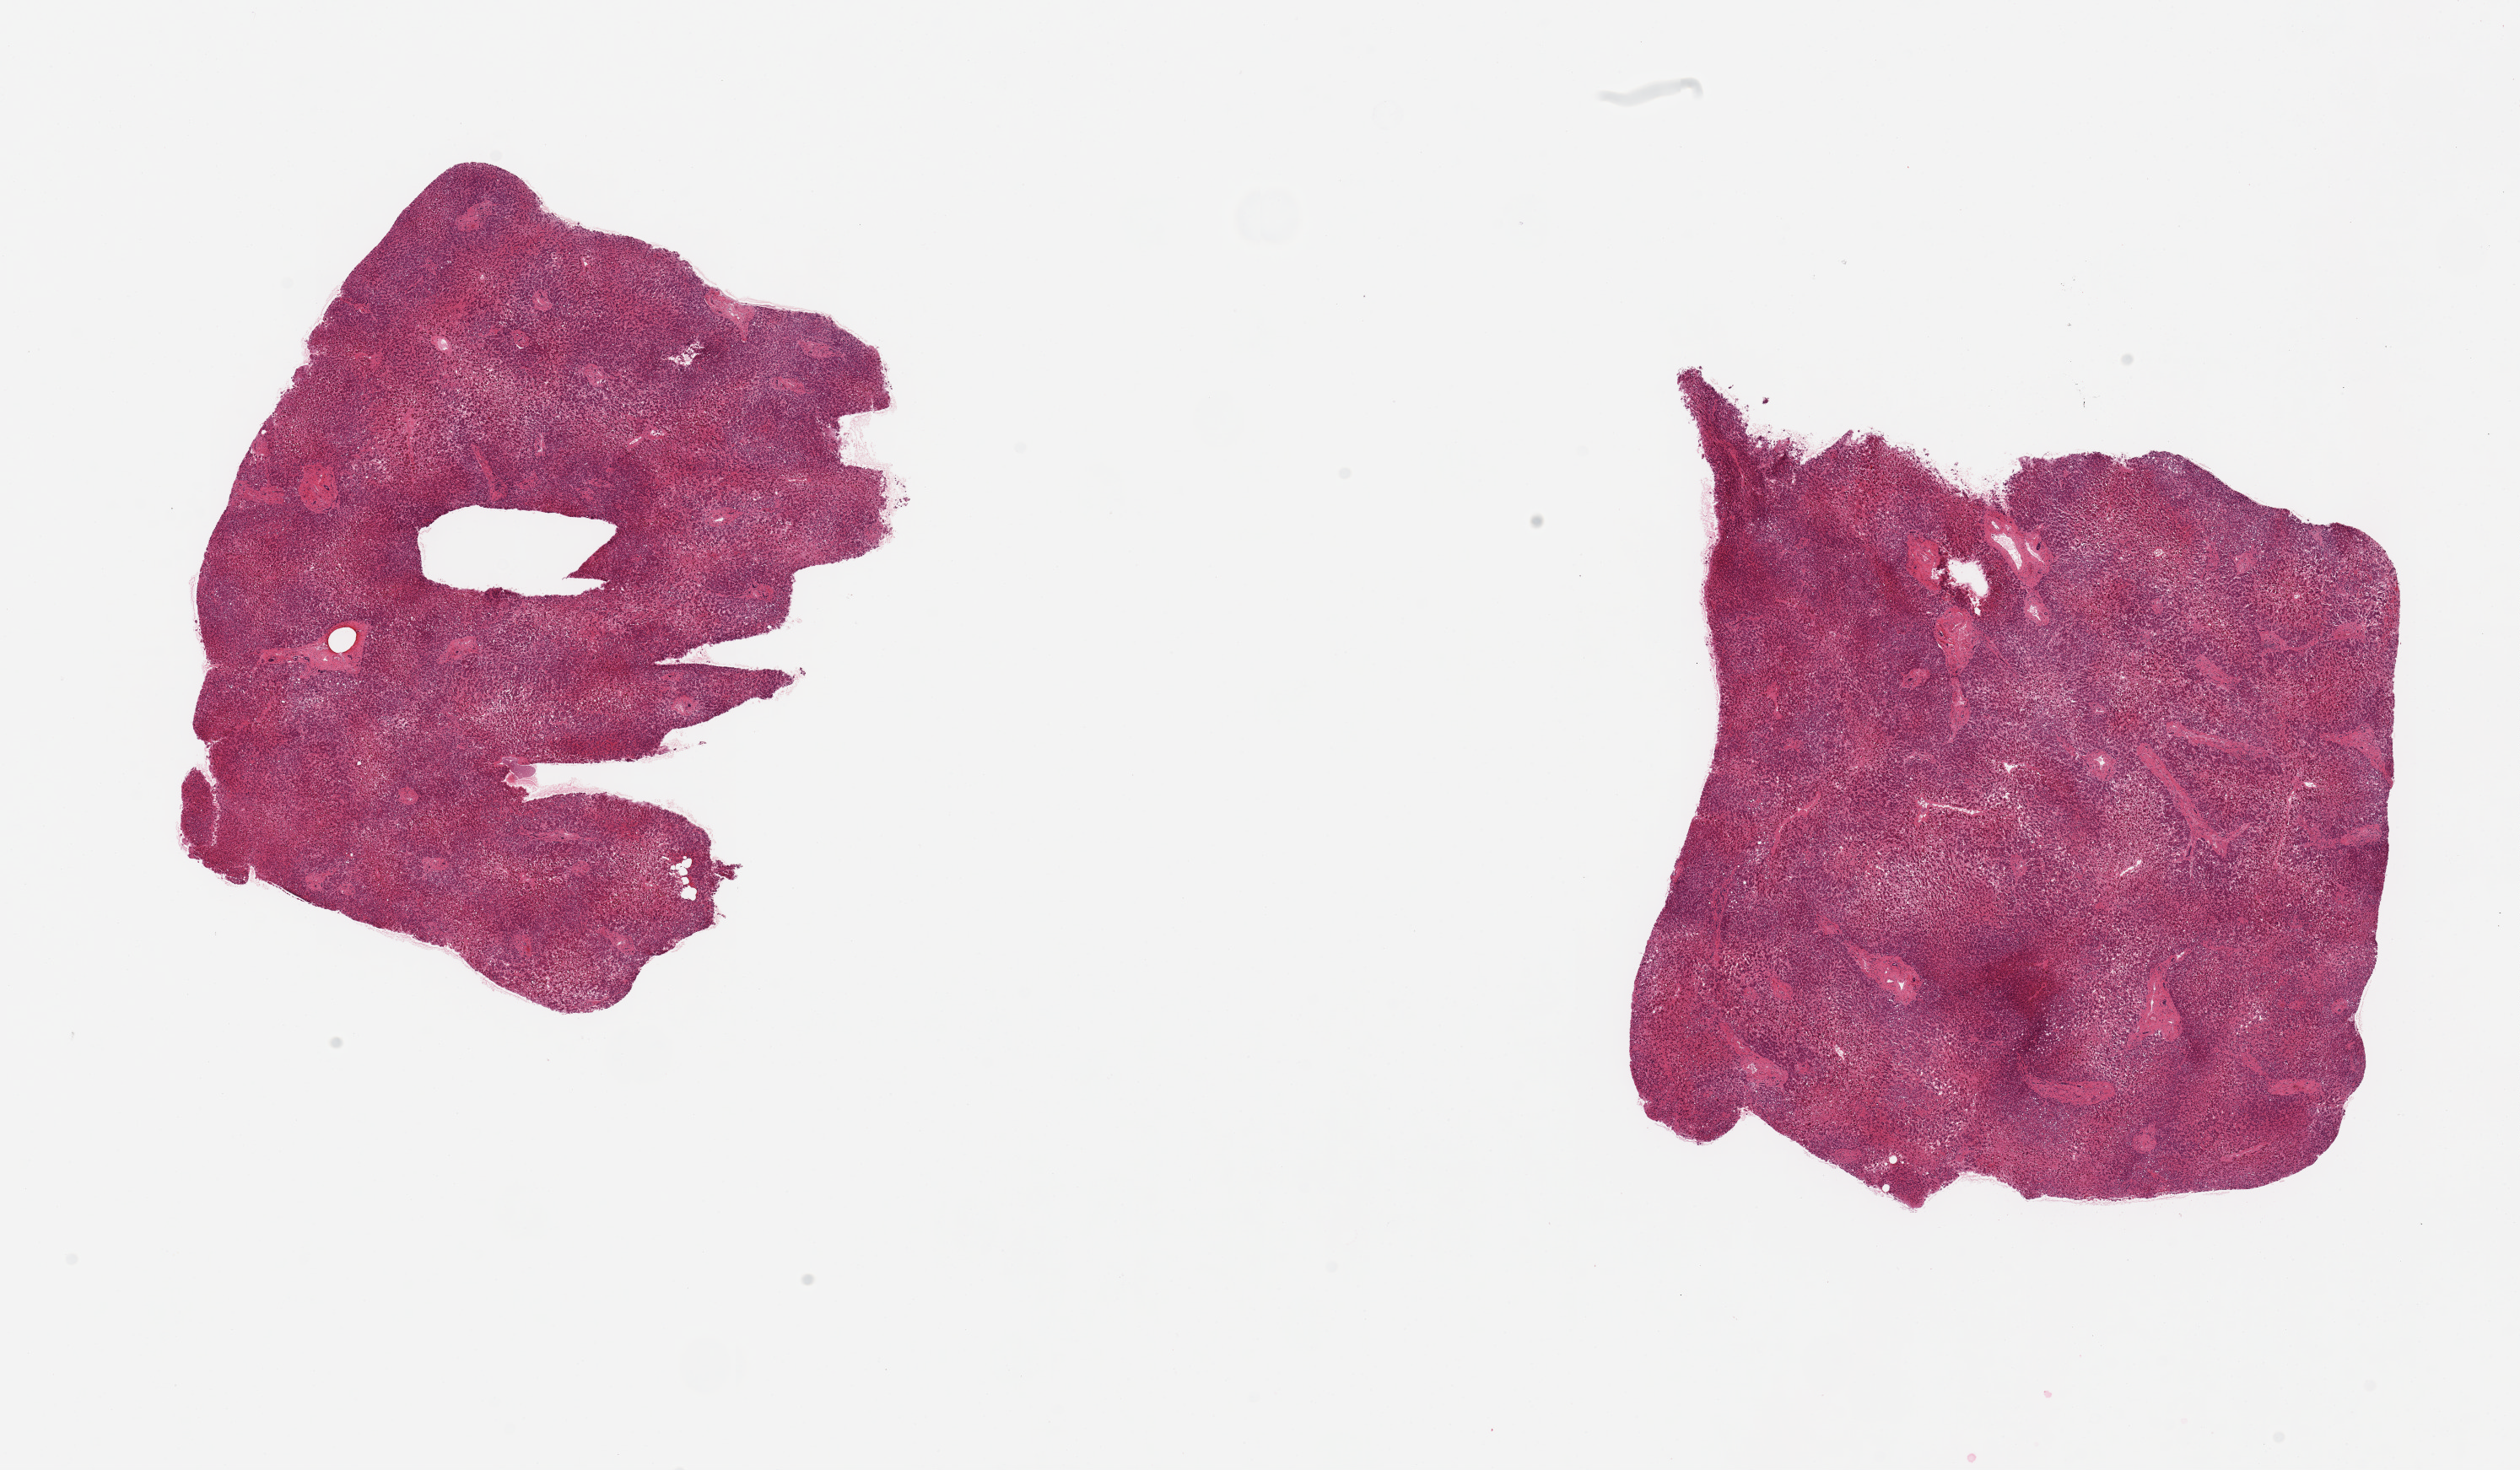
Hematoxylin and eosin (H&E) whole-slide image, brightfield — whole scanned area (about 23.6 x 13.8 mm, from a 20x scan) shown as a low-resolution overview. PAXgene-fixed, paraffin-embedded tissue. Sampled site (target tissue): liver. Tissue donor sample.
Reviewer comment on this tissue sample: 2 pieces;10% macrovesicular steatosis; central congestion and degeneration.